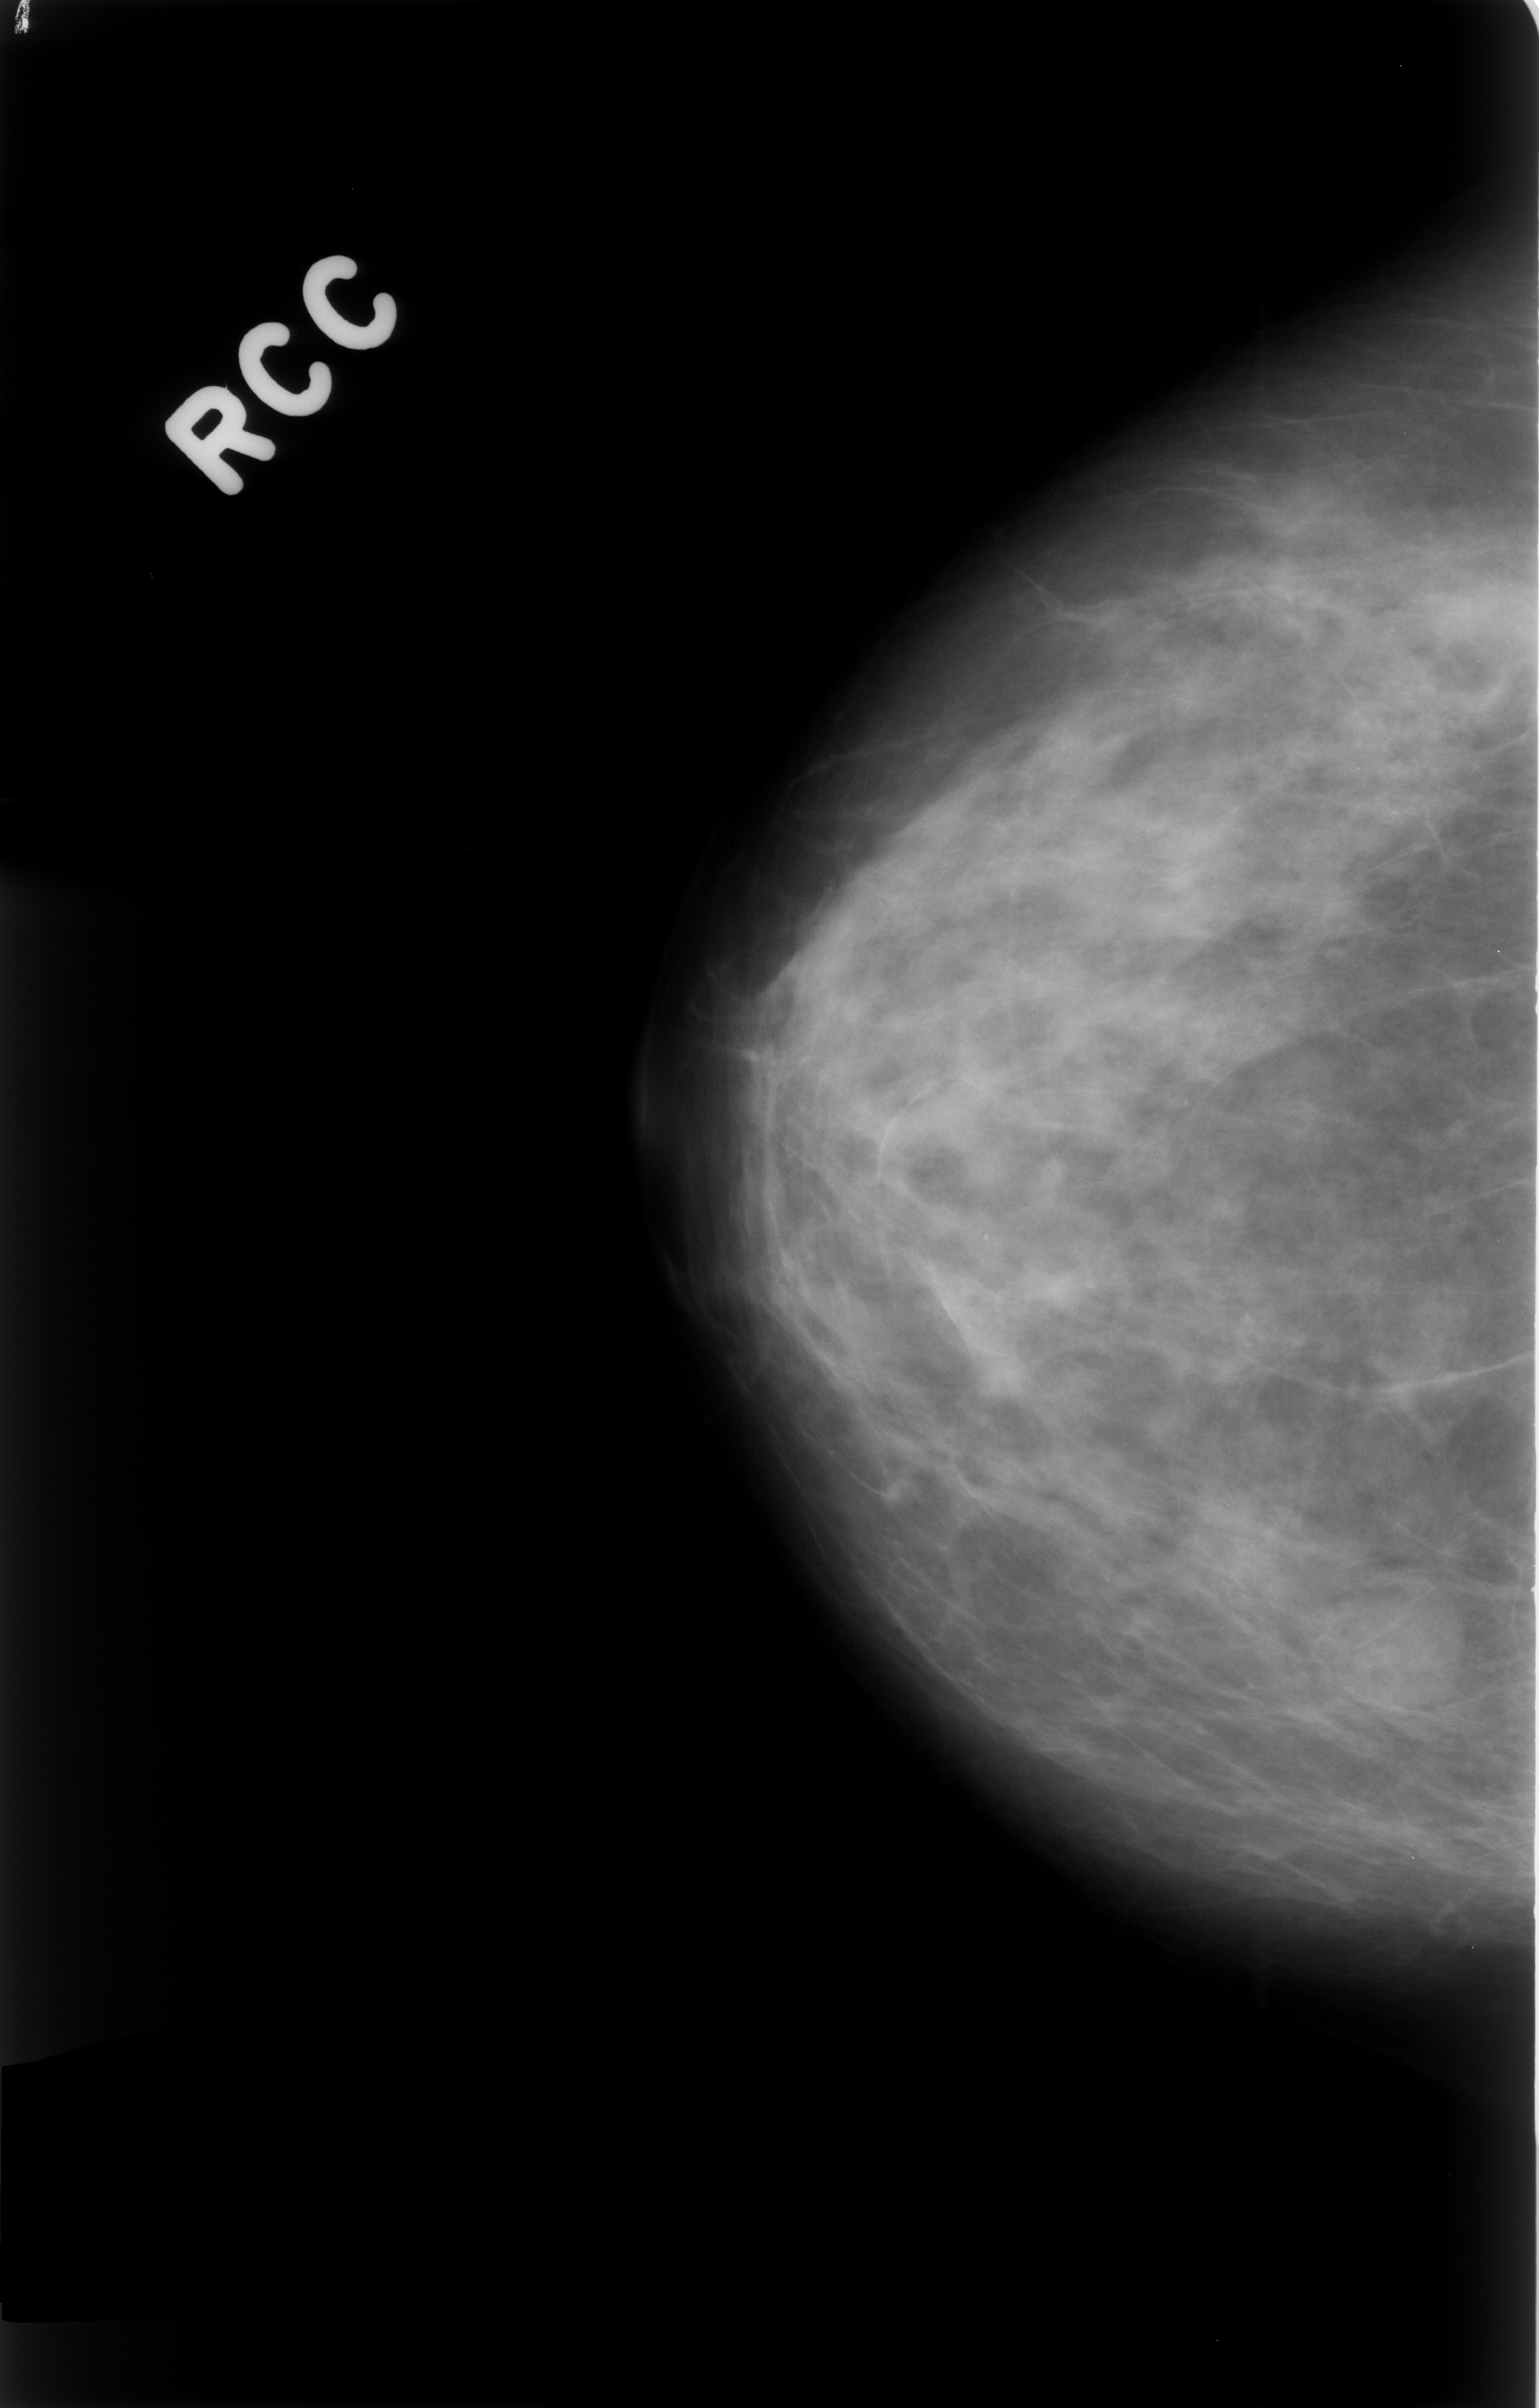
Digitized screen-film mammogram; right breast; craniocaudal (CC) view; BI-RADS breast density category 2 (scale 1–4); 1539 × 2408 image matrix.
Marked abnormalities (boxes around the expert regions of interest):
- mass, shape round, margins circumscribed; BI-RADS assessment category 4; pathology (as recorded): benign: bounding box (x1, y1, x2, y2) in pixels: (1296, 1567, 1455, 1732)